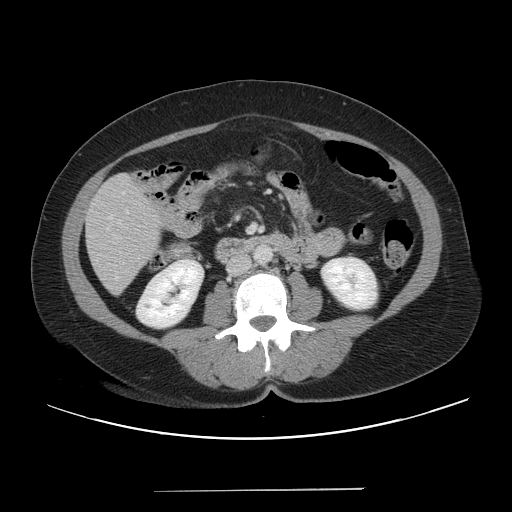
Contrast-enhanced abdominal CT, one axial slice. Slice 11 of 56 in the series (ordered by position). Intravenous contrast given. Soft-tissue window (W 400 / L 40 HU). 512 × 512 image matrix. Female patient, age 54 years. From the clinical record (not read from this slice): diagnosis: colorectal cancer liver metastases, imaged before liver resection; multiple liver metastases: yes; largest metastasis: 3.2 cm; disease in both lobes: yes.
Structures marked on this image (expert manual segmentation):
- liver: box from (x=86, y=173) to (x=161, y=294) px
- portal vein (with intrahepatic branches): (x=251, y=226)–(x=255, y=232)